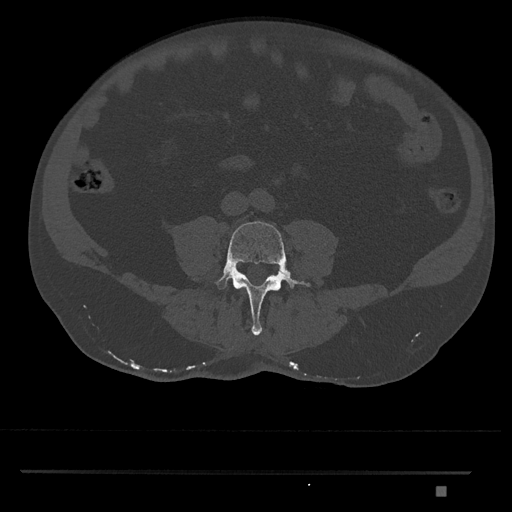
CT including the spine, one axial slice. Position 615 of 1134 along the scan axis. Reconstruction kernel Br40s/3. 120 kVp. Bone window (W 1800 / L 400 HU). 0.5 mm slice thickness. 512 × 512 image matrix, field of view 429 × 429 mm. Male patient, age 65 years. Case-level facts recorded for this patient, not image findings: primary cancer: prostate.
Structures marked on this image (semi-automatically segmented with operator editing):
- L4 vertebra: bounding box [x1, y1, x2, y2] px = [215, 221, 311, 336]